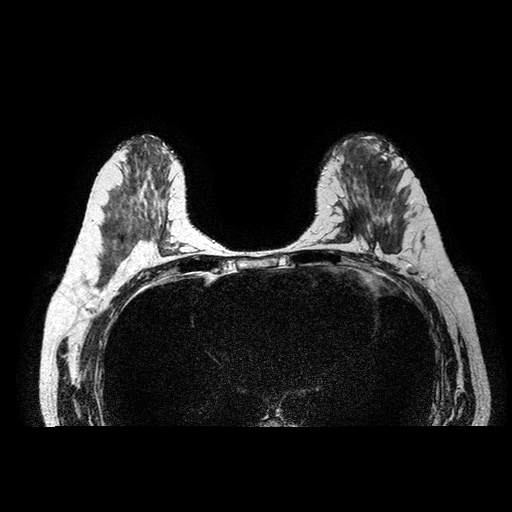
Breast MRI examination; 2 images, each one mid-volume slice chosen by position. Patient in her 40s.
Image 1: axial T2-weighted / STIR image, series "T2W_TSE SENSE", slice 43 of 84, 2 mm slice thickness.
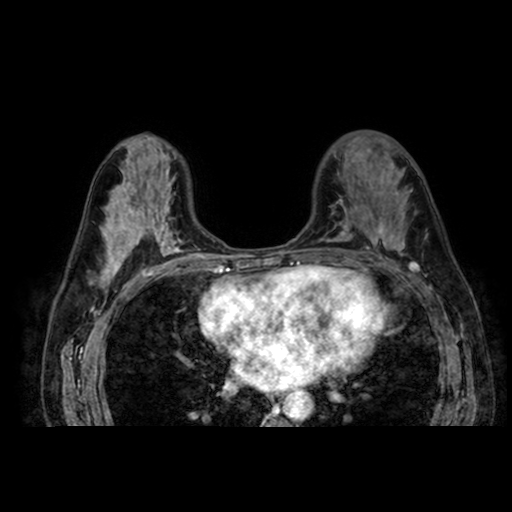
Image 2: post-contrast dynamic axial slice, slice 45 of 88, dynamic phase 5 of 8.
Pathology recorded for this patient (not read from these images): pathology diagnosis: intraductal CA (left breast); receptor status (as recorded): ER neg, PR neg, HER2 pos; Ki-67 (as recorded): high prolif.